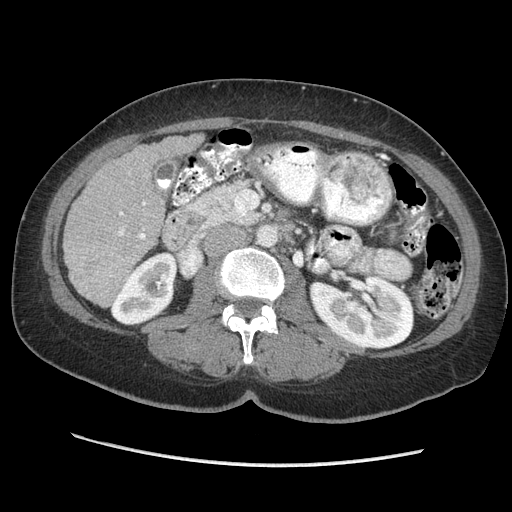
Contrast-enhanced abdominal CT (liver protocol), one axial slice; slice 106 of 170 in the series (ordered by position); reconstruction kernel STANDARD; 140 kVp; soft-tissue window (W 400 / L 40 HU); 2.5 mm slice thickness; 512 × 512 image matrix. Case-level facts recorded for this patient, not image findings: diagnosis: hepatocellular carcinoma (patient treated with transarterial chemoembolisation; whether this scan precedes or follows treatment is not stated here); TNM stage (as recorded): Stage-II; Child-Pugh class: A; tumour differentiation: no biopsy; tumour nodularity: multinodular.
Outlined on this slice (semi-automatically segmented with operator editing):
- liver parenchyma outside the tumour (the mass and vessels are separate outlines, so this box may not span the whole liver): bounding box (x1, y1, x2, y2) in pixels: (62, 134, 204, 306)
- liver vessels: (119, 202, 146, 239)